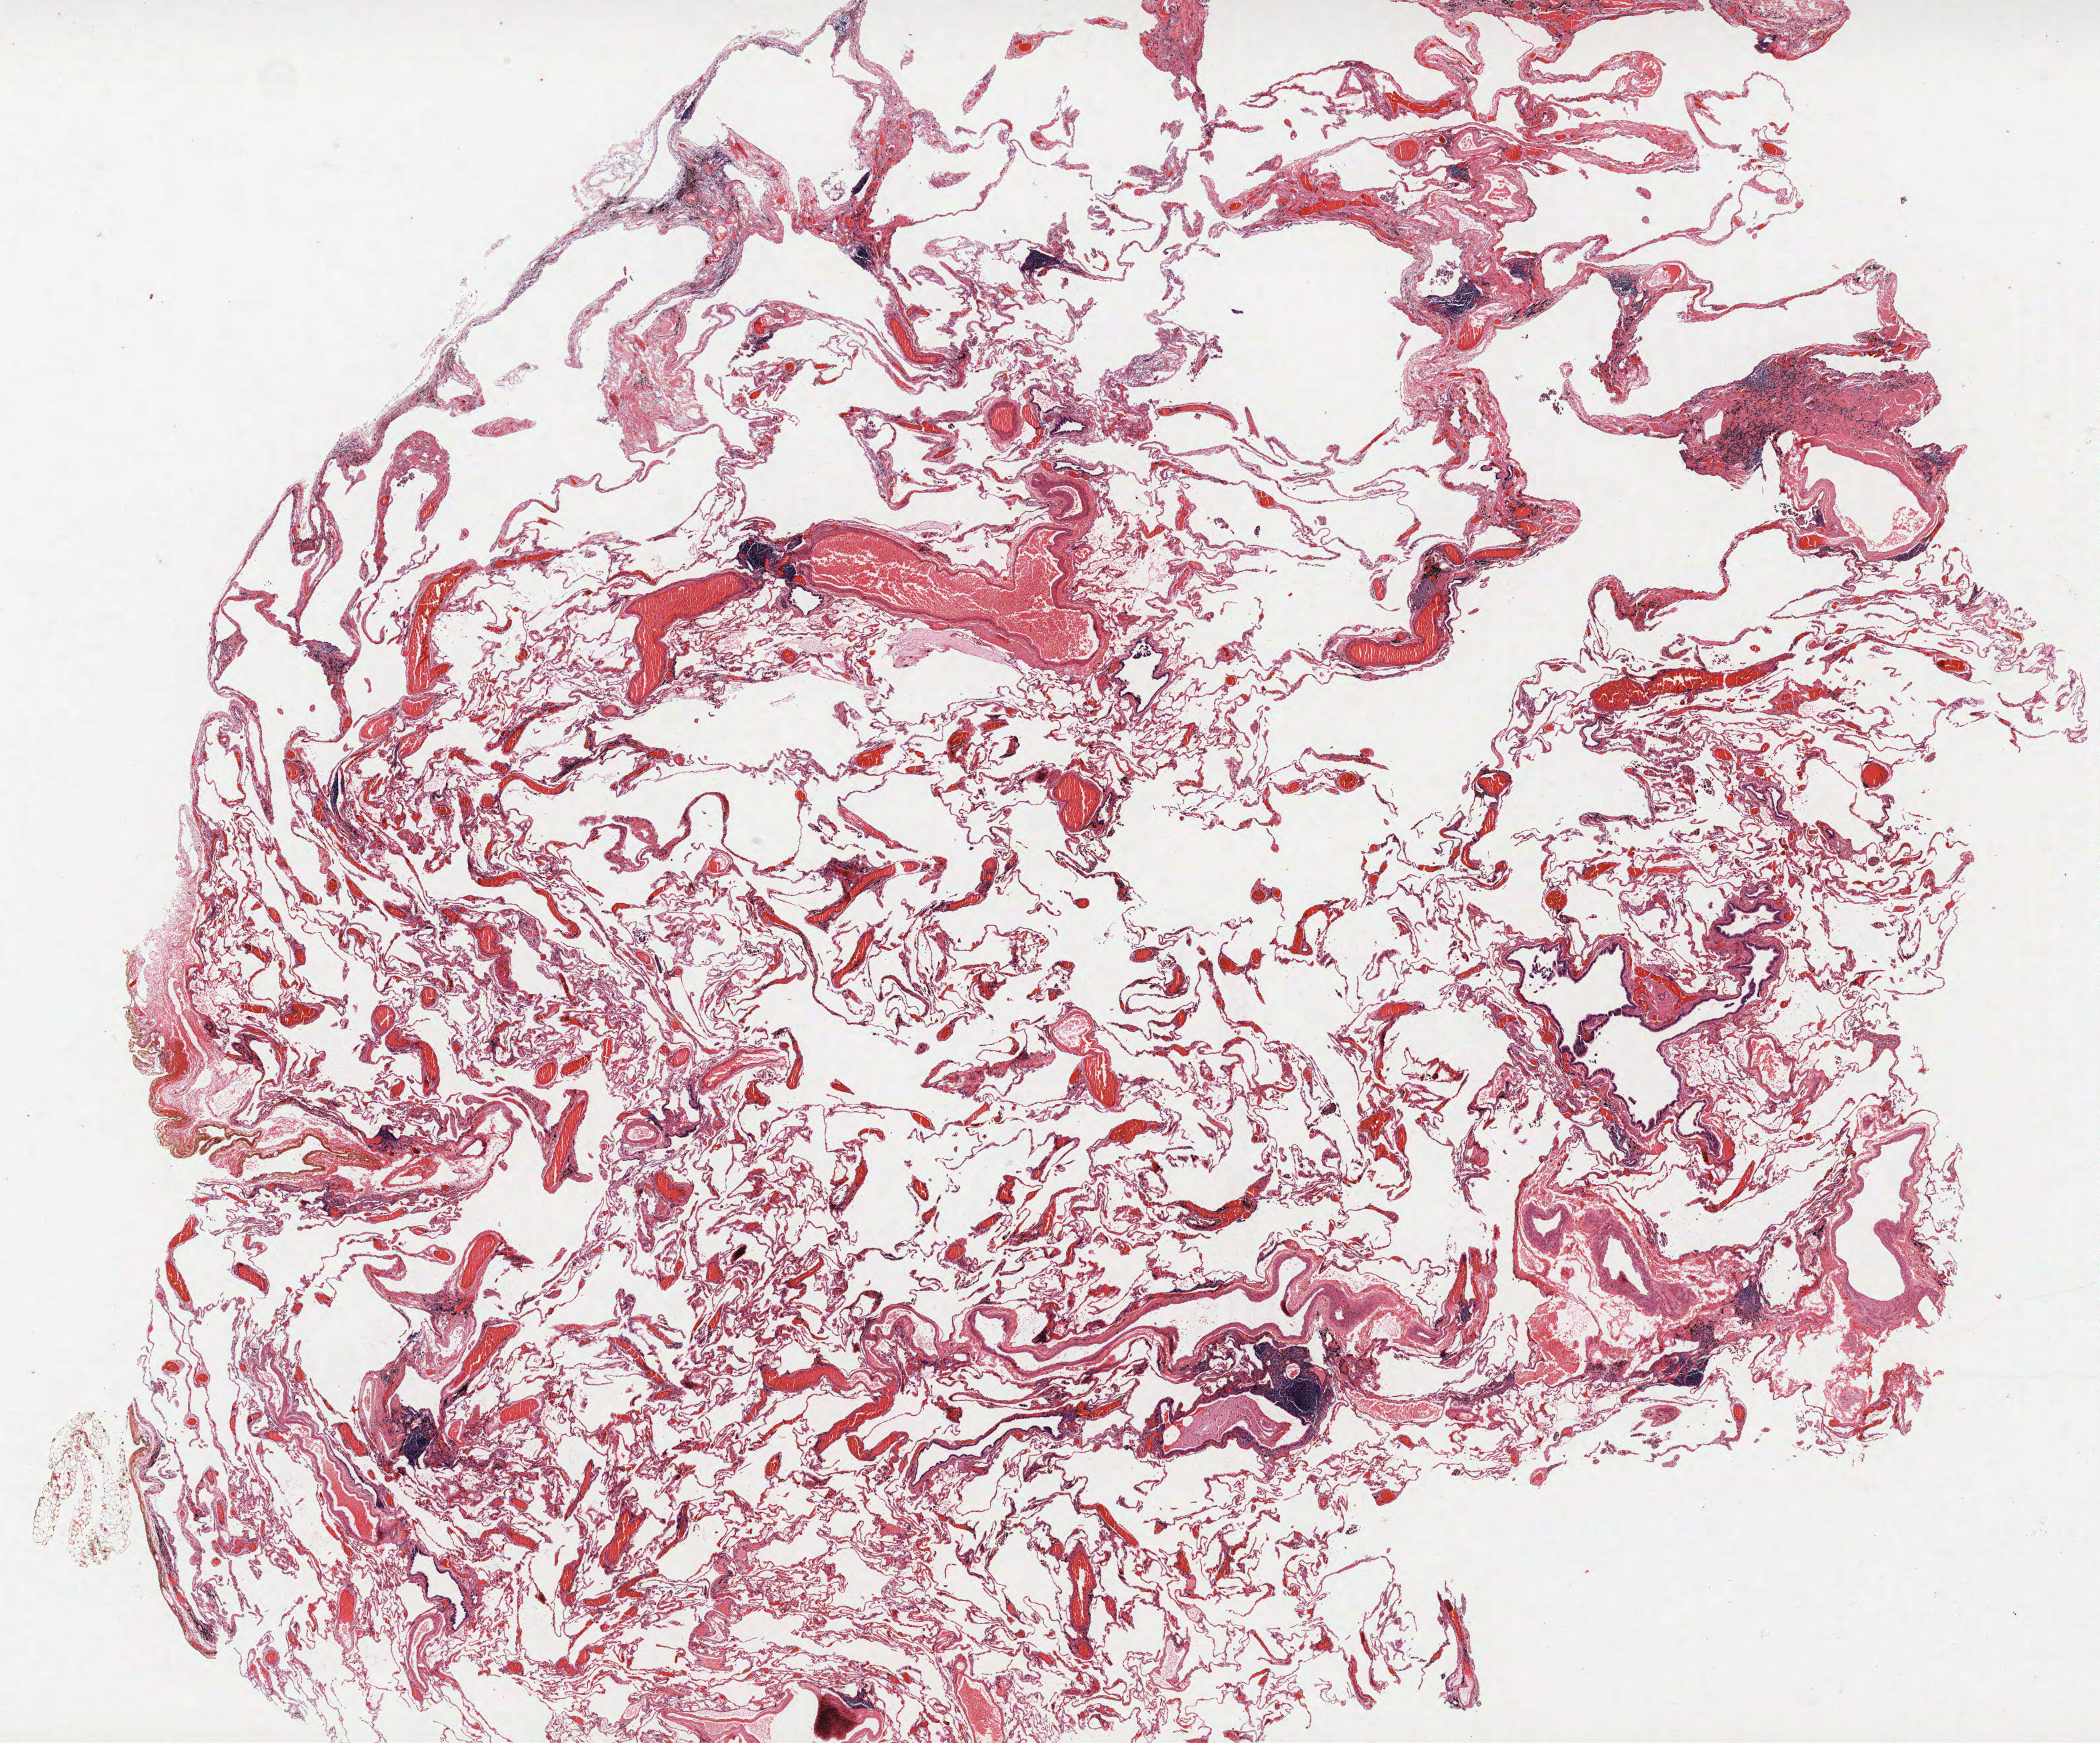
Whole-slide histology image, Hematoxylin and eosin (H&E) stained — low-resolution overview of the scanned area, about 25.2 x 20.9 mm (acquisition: 40x scan), FFPE section, lung tissue. Female patient, aged 62 at enrolment. Current smoker at enrolment. Grade: moderately differentiated (G2).
Stage (AJCC 6th edition): IA. Primary tumour location (clinical record): right upper lobe. Participant's lung-cancer diagnosis: Adenocarcinoma, NOS (ICD-O-3 8140/3). ICD-O-3 topography: upper lobe of lung (C34.1). Tumour size (pathology): 15 mm.